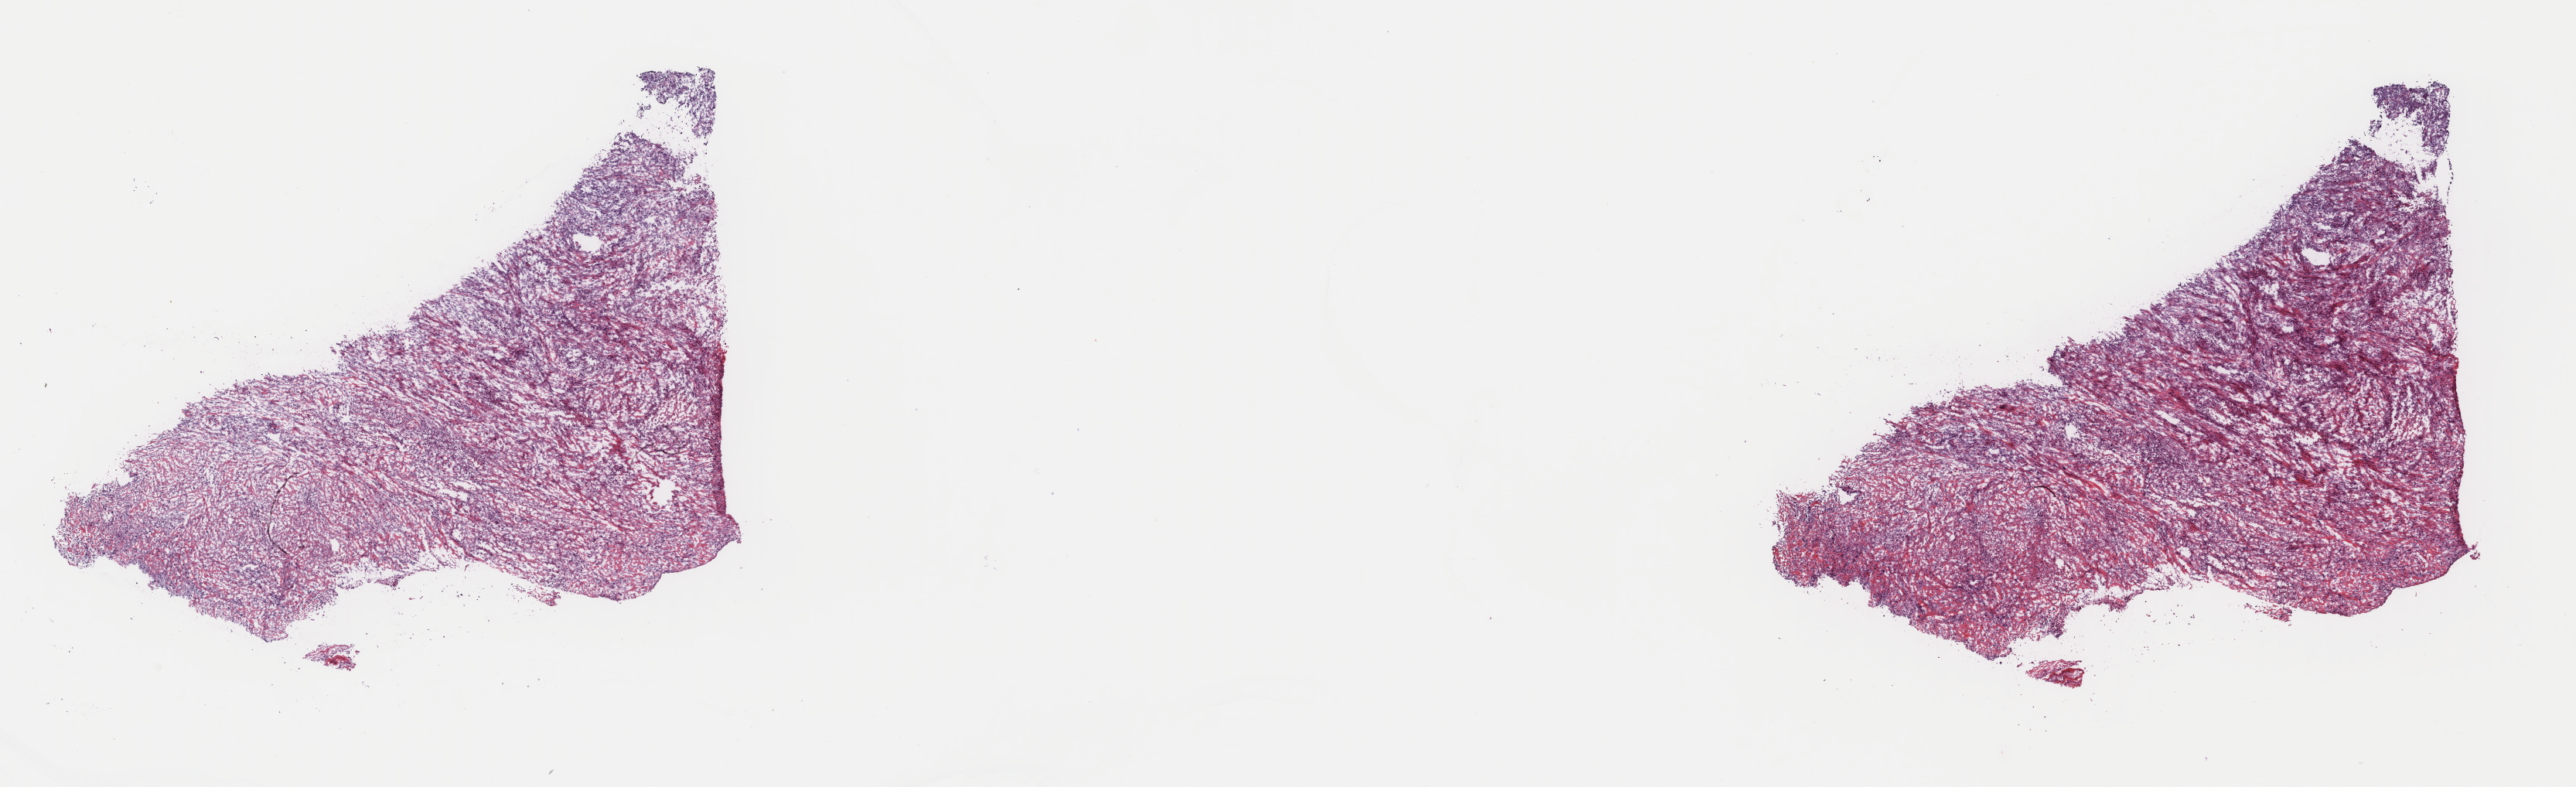
Whole-slide histology image, H&E — shown as a low-resolution overview of the whole scanned area (about 26.4 x 8.1 mm); frozen section from the top of the tissue portion; sample: primary tumour, connective, subcutaneous and other soft tissues. Patient: male, age at initial diagnosis 67 years. Pathologist review of this section (percent, as recorded): tumour cells 95%, tumour nuclei 90%, normal cells 0%, stromal cells 0%, necrosis 5%. Inflammatory infiltration, as recorded: lymphocyte infiltration 0%, monocyte infiltration 0%, neutrophil infiltration 0%.
* pathologic diagnosis: Leiomyosarcoma, NOS